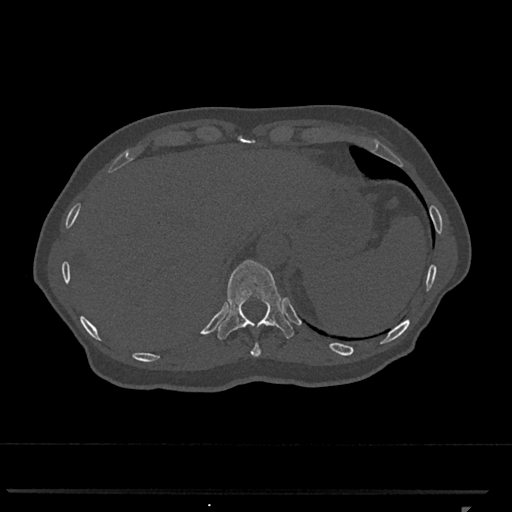
CT including the spine, one axial slice; position 528 of 793 along the scan axis; bone window (W 1800 / L 400 HU); 0.5 mm slice thickness; 512 × 512 image matrix. Female patient, age 62 years. Case-level facts recorded for this patient, not image findings: primary cancer: renal.
Annotated regions visible in this slice (semi-automatically segmented with operator editing):
- T10 vertebra: bounding box <250,343,261,357> (left, top, right, bottom; pixels)
- T11 vertebra: <217,260,294,340>